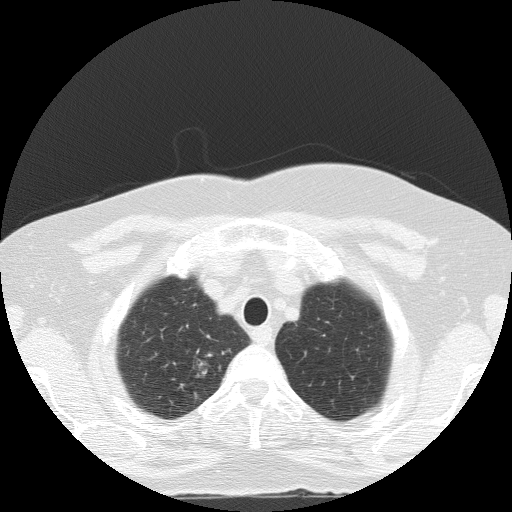
Low-dose screening chest CT, axial slice; baseline annual screen; lung window (W 1500 / L -600 HU); 120 kVp; 512 × 512 image matrix. Female, age 56 years at enrolment.
• Expert-annotated lung lesion, box from (x=174, y=345) to (x=229, y=389) px.
• The screening reader recorded 2 non-calcified nodules or masses ≥4 mm on this exam; which of them this box marks is not recorded.
• Later outcome: lung cancer diagnosed 24 days after this screen — adenocarcinoma, NOS, right upper lobe, poorly differentiated (G3), stage IA (AJCC 6th edition), 20 mm at pathology.